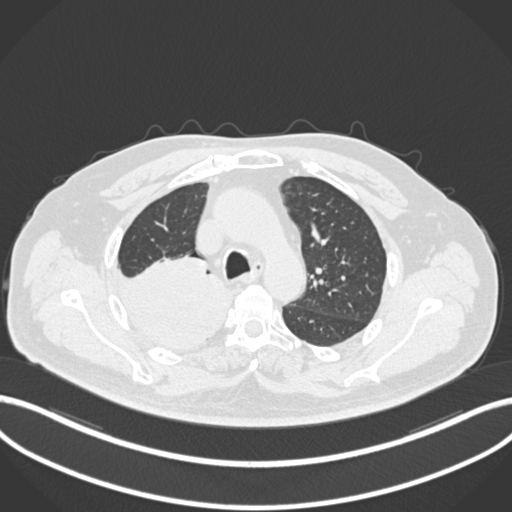
Chest CT, one axial slice; slice 149 of 218 in the series (ordered by position); 120 kVp; lung window (W 1500 / L -600 HU); 512 × 512 image matrix, field of view 400 × 400 mm. Patient: male, 68 years. From the clinical record (not read from this slice): clinical TNM (as recorded): T2a N0 M0.
Structures marked on this image (rectangle marked by the reading radiologist):
- lung tumour (recorded histology: adenocarcinoma): box from (x=114, y=255) to (x=234, y=349) px